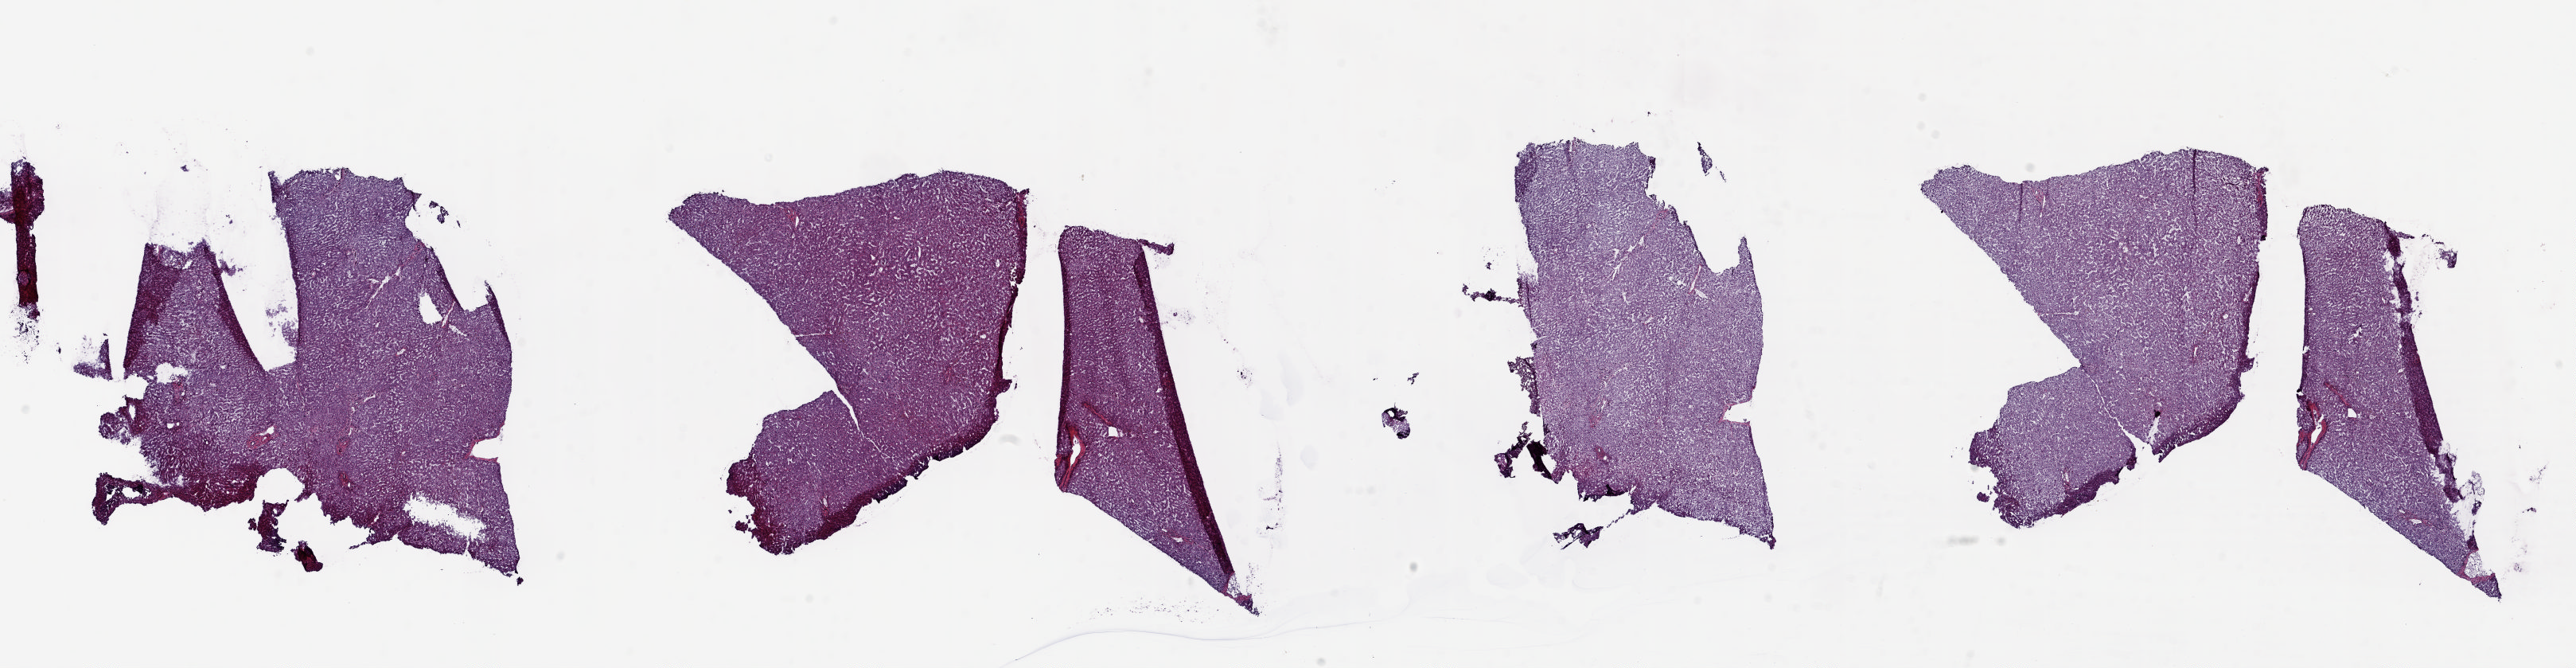
Whole-slide histology image, H&E-stained — low-resolution overview of the scanned area, about 25.7 x 6.7 mm, frozen section from the top of the tissue portion, solid tissue normal (non-tumour tissue) sample from the liver. Patient: female, age at initial diagnosis 77 years. Pathologist review of this section (percent, as recorded): tumour cells 0%, tumour nuclei 0%, normal cells 95%, stromal cells 5%, necrosis 0%. Inflammatory infiltration, as recorded: lymphocyte infiltration 1%, monocyte infiltration 0%, neutrophil infiltration 0%.
This section: solid tissue normal sample (biorepository sample class). Patient diagnosis: Hepatocellular carcinoma, NOS.